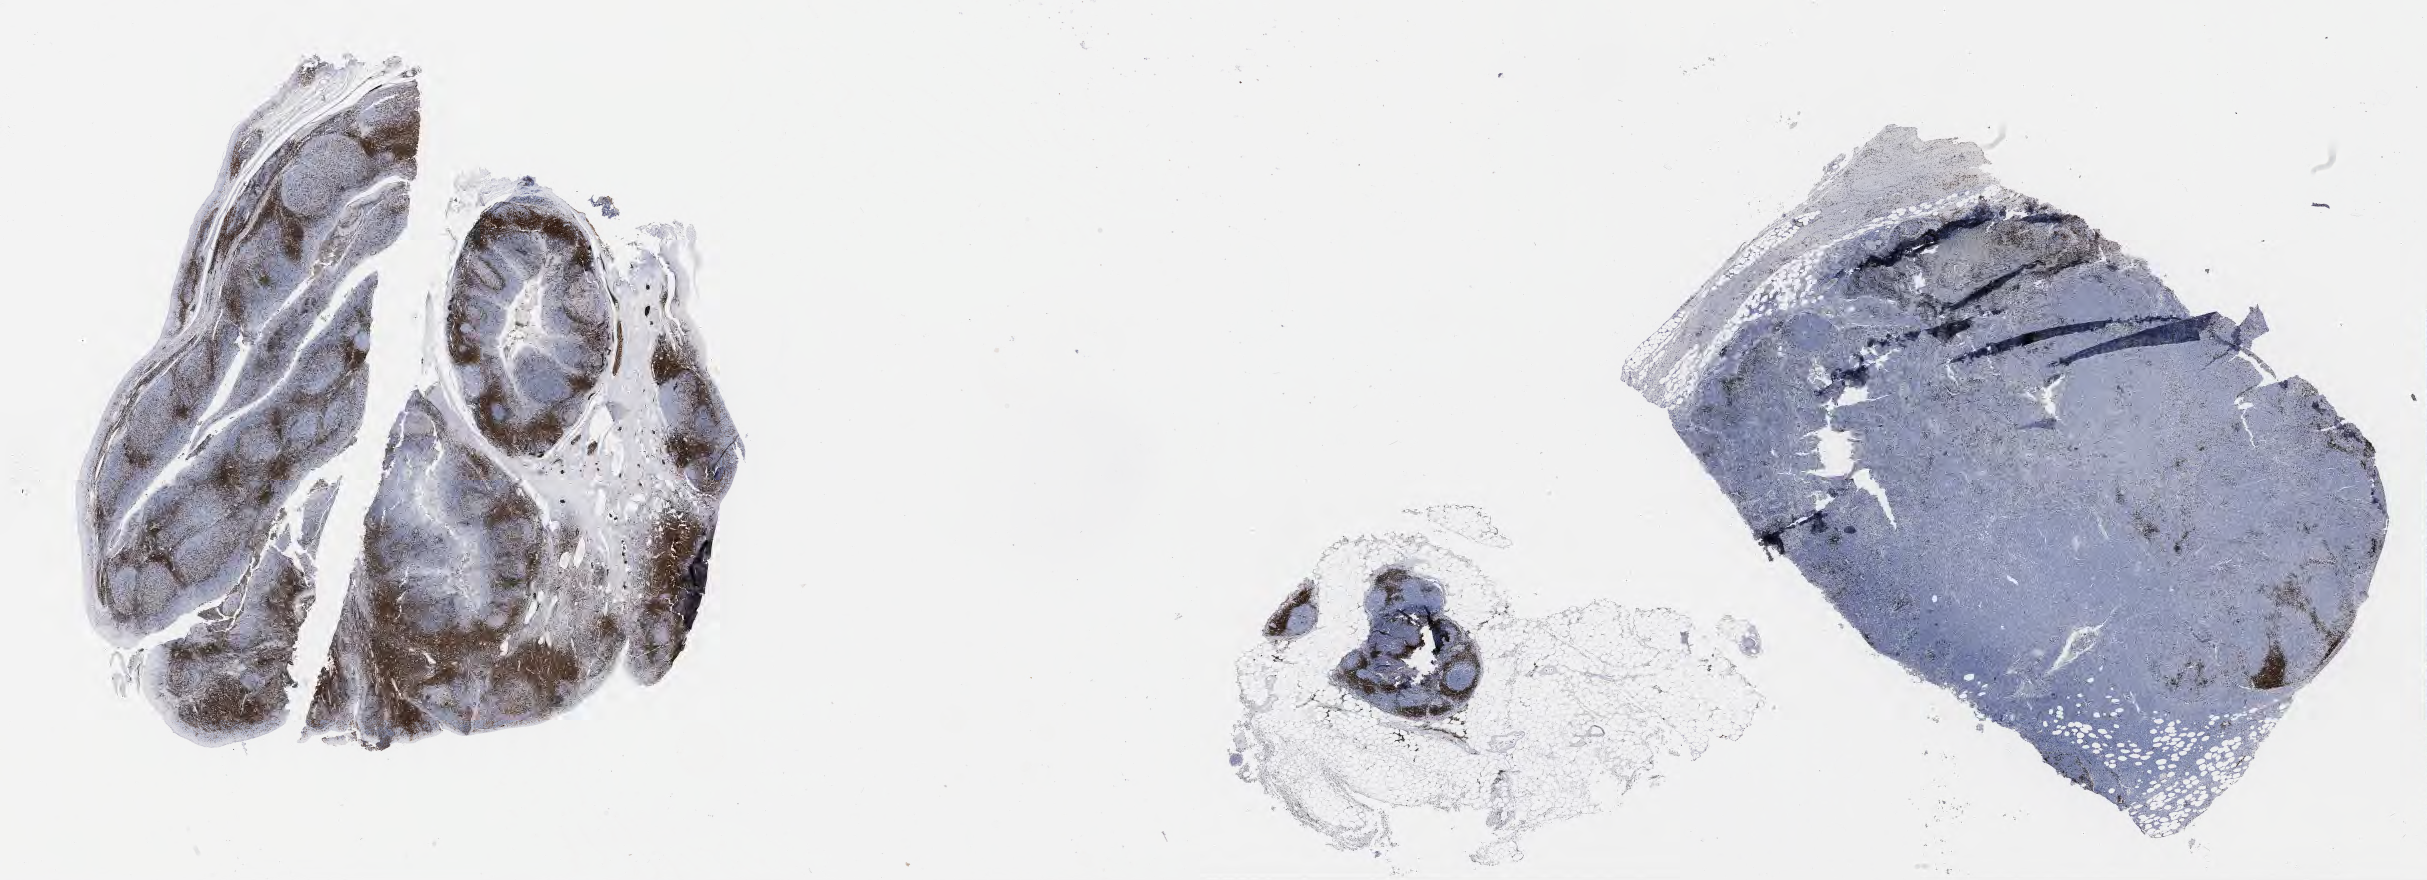
Immunohistochemistry (IHC) whole-slide image stained for CD3 — whole scanned area (about 39.2 x 14.2 mm) shown as a low-resolution overview, tumor tissue. Patient: male, 40 years old.
Diagnosis: Burkitt lymphoma, NOS.